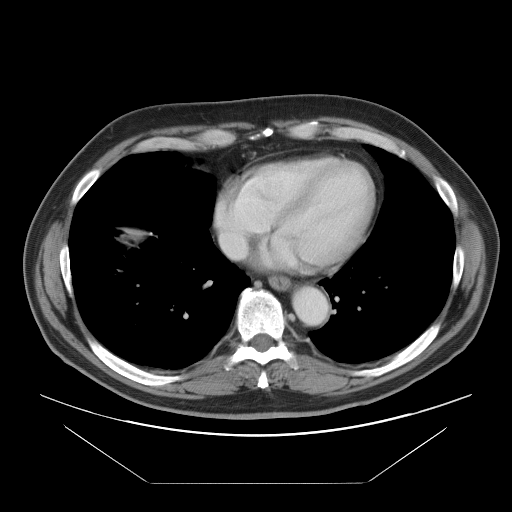
Contrast-enhanced abdominal CT, one axial slice; position 93 of 97 along the scan axis; soft-tissue window (W 400 / L 40 HU); 5 mm slice thickness; 512 × 512 image matrix. Male patient, age 62 years. From the clinical record (not read from this slice): diagnosis: colorectal cancer liver metastases, imaged before liver resection; multiple liver metastases: no; largest metastasis: 7 cm; chemotherapy before resection: yes.
Annotated regions visible in this slice (expert manual segmentation):
- hepatic veins: bounding box [x1, y1, x2, y2] px = [217, 201, 247, 260]